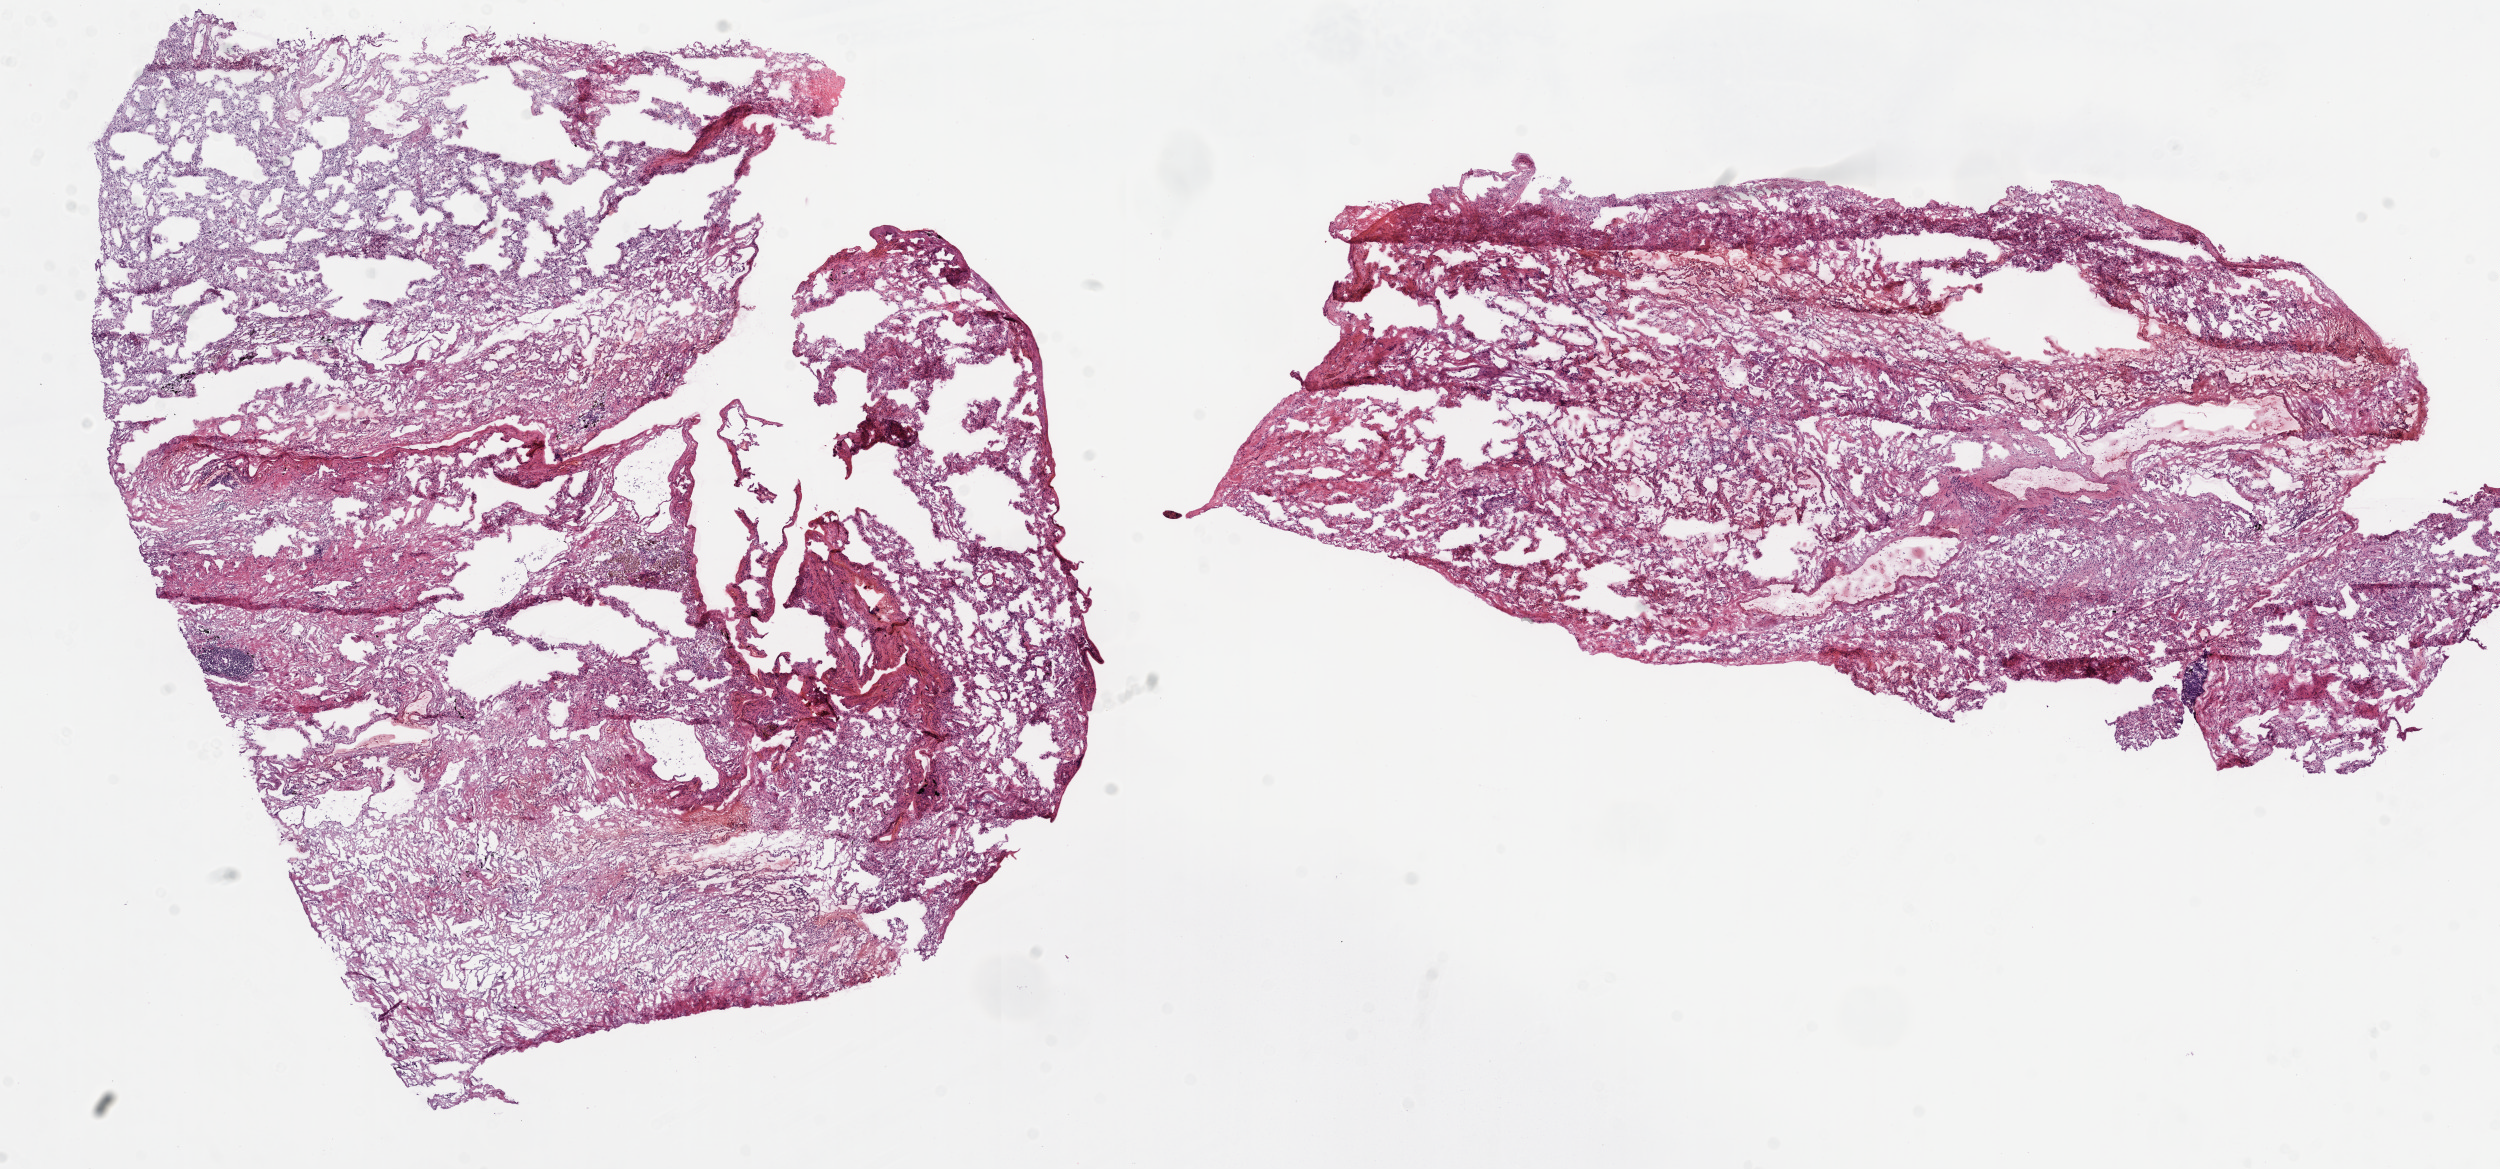
Whole-slide histology image, H&E — a low-resolution overview of the entire scanned area, about 20.1 x 9.4 mm (from a 20x scan). Frozen section from the top of the tissue portion. Solid tissue normal (non-tumour tissue) sample from the lung. Patient: female, age at initial diagnosis 63 years.
This section: solid tissue normal sample (biorepository sample class). Patient diagnosis: Squamous cell carcinoma, small cell, nonkeratinizing.